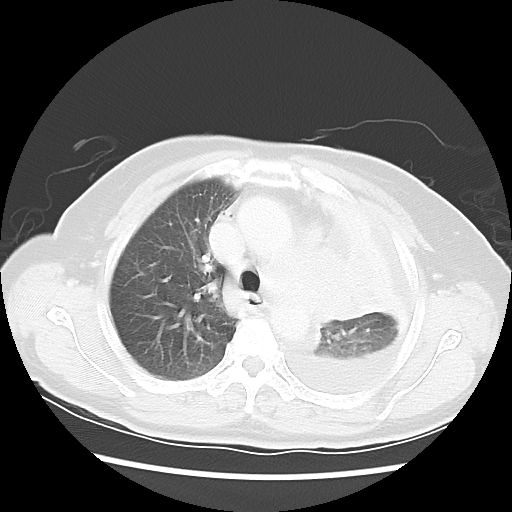
Chest CT, one axial slice. Slice 38 of 52 in the series (ordered by position). Reconstruction kernel LUNG. 120 kVp. Lung window (W 1500 / L -600 HU). 5 mm slice thickness. 512 × 512 image matrix, field of view 336 × 336 mm. Female patient, age 72 years. From the clinical record (not read from this slice): clinical TNM (as recorded): T4 N3 M1b; histopathological grade: G3.
Annotated regions visible in this slice (bounding box drawn by a radiologist):
- lung tumour (recorded histology: large cell carcinoma): bounding box (x1, y1, x2, y2) in pixels: (271, 239, 388, 333)